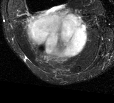
MRI of an extremity soft-tissue mass, one axial slice. Slice 31 of 44 in the series (ordered by position). T2-weighted fat-saturated. MR volume resampled by the dataset authors to the PET/CT grid (not the native acquisition matrix). 114 × 103 image matrix, field of view 111 × 101 mm. Female patient. Case-level facts recorded for this patient, not image findings: histological type: liposarcoma; site of the primary tumour: right thigh.
Annotated regions visible in this slice (expert contour drawn on MRI and transferred to this co-registered scan by the dataset authors):
- gross tumour volume (mass): box from (x=24, y=7) to (x=89, y=63) px